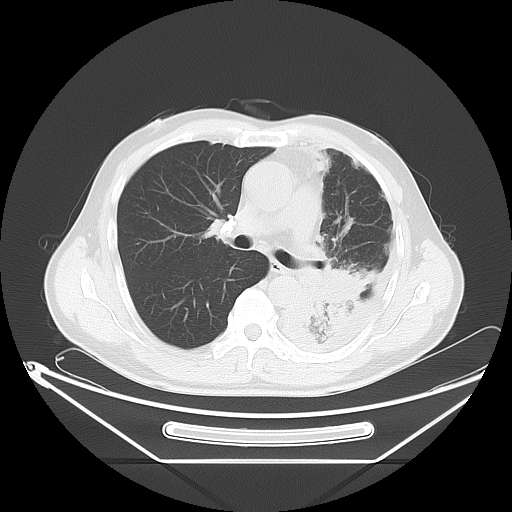
Chest CT, one axial slice. Slice 38 of 63 in the series (ordered by position). Reconstruction kernel LUNG. 120 kVp. Lung window (W 1500 / L -600 HU). 5 mm slice thickness. 512 × 512 image matrix. Patient: male, 60 years. Case-level facts recorded for this patient, not image findings: clinical TNM (as recorded): T4 N1 M1.
Annotated regions visible in this slice (bounding box drawn by a radiologist):
- lung tumour (recorded histology: adenocarcinoma): bounding box (x1, y1, x2, y2) in pixels: (295, 254, 369, 322)